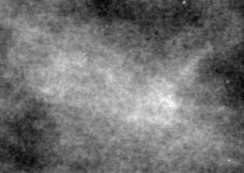
Region of interest cut from a scanned film mammogram (one marked finding); right breast; MLO view.
Finding: mass, shape oval, margins ill defined; BI-RADS assessment category 4; pathology result (as recorded, not read from the image): benign.